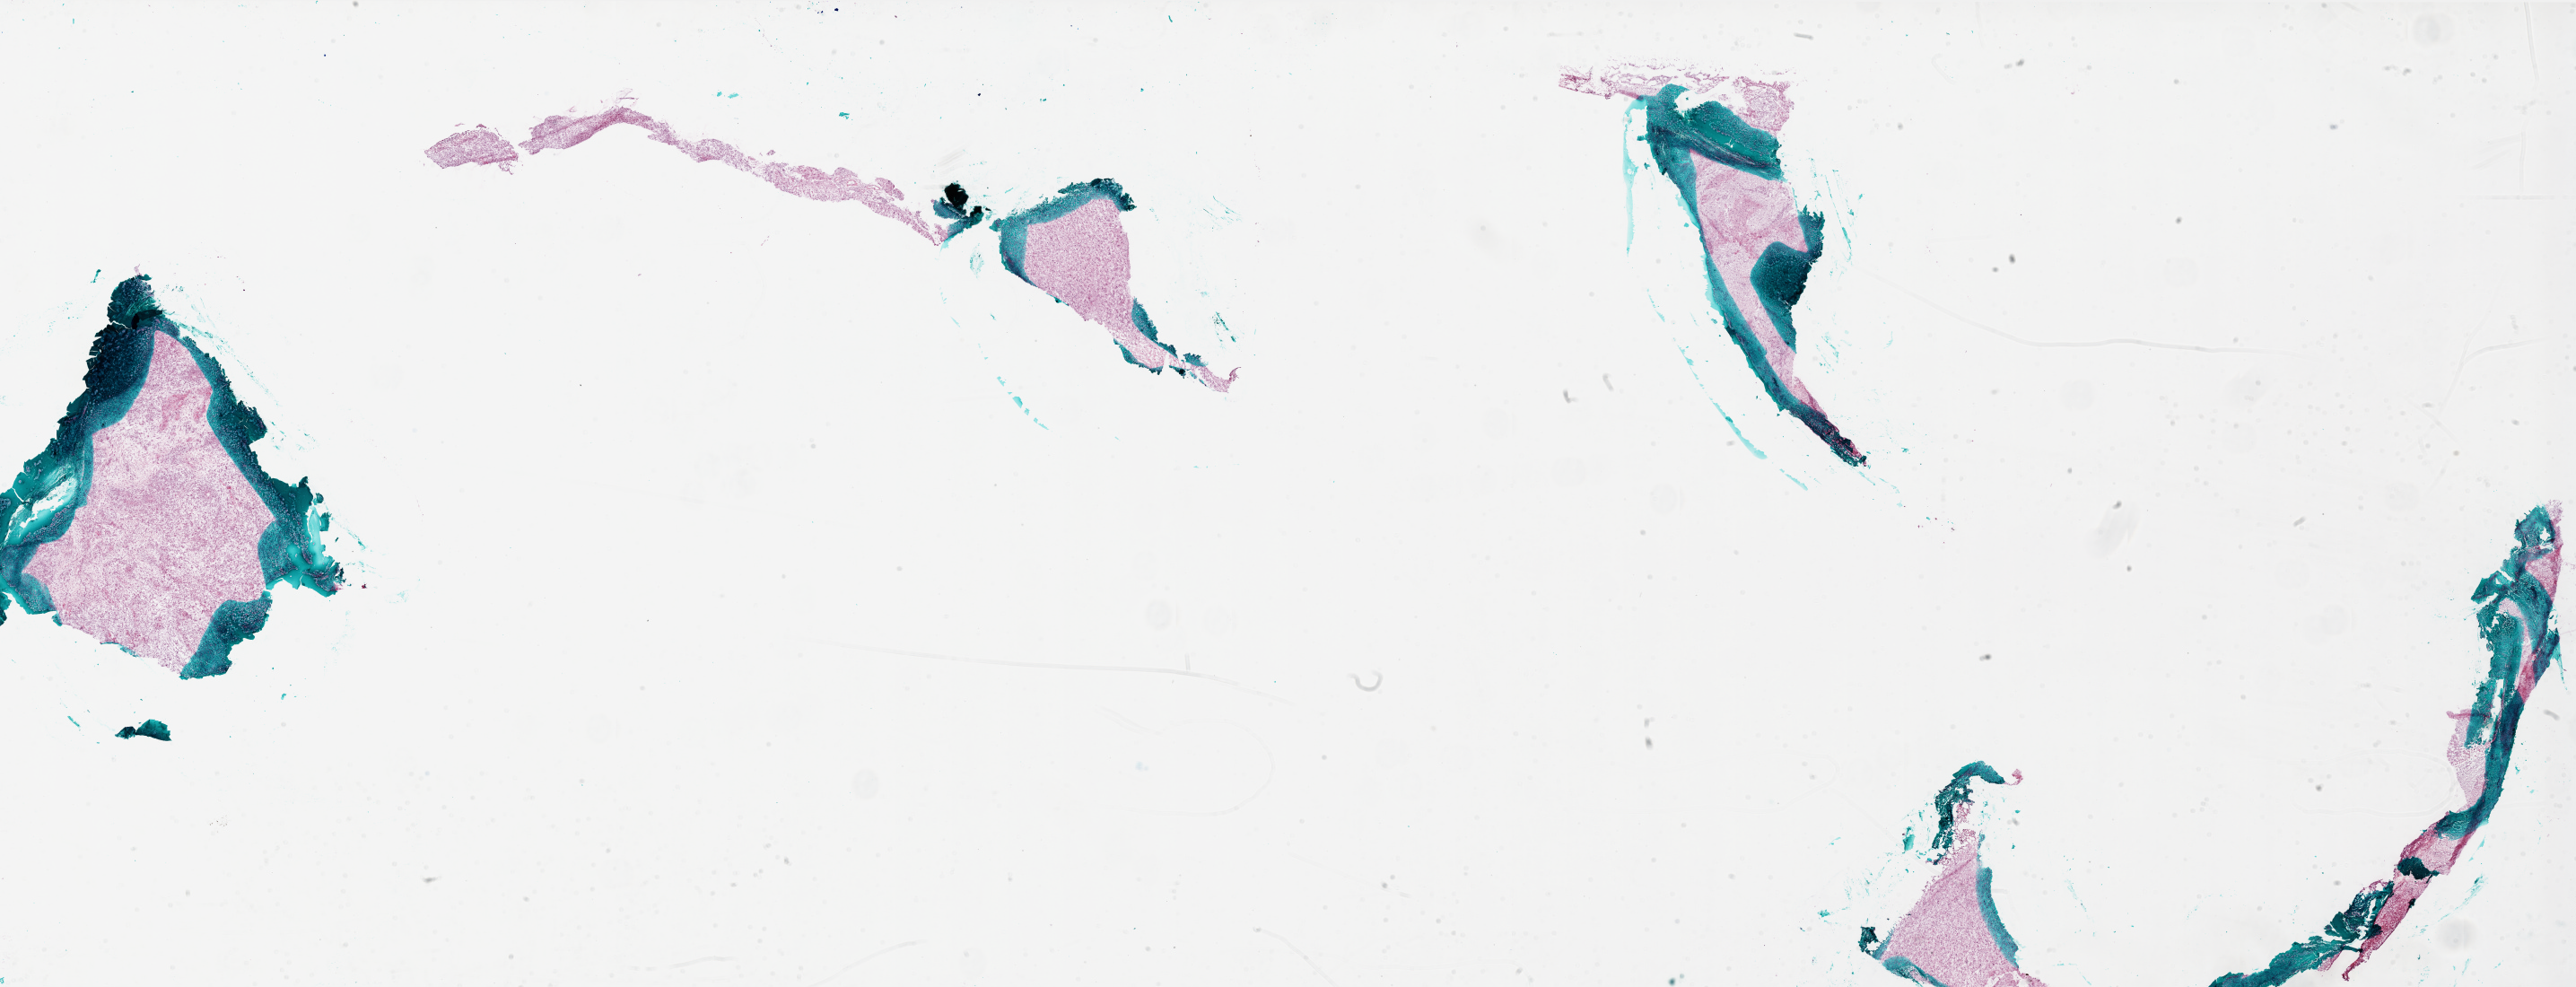
H&E whole-slide image — a low-resolution overview of the entire scanned area, about 46.0 x 17.6 mm (from a 20x scan). Frozen section from the bottom of the tissue portion. Brain, primary tumour sample. Male patient; age at initial diagnosis 59 years. Pathologist review of this section (percent, as recorded): tumour cells 90%, tumour nuclei 100%, normal cells 0%, stromal cells 0%, necrosis 10%.
Pathologic diagnosis: Glioblastoma.